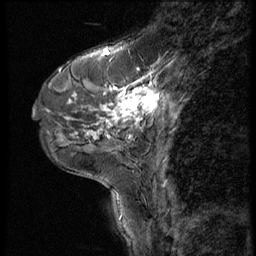
Breast MRI (dynamic contrast-enhanced), one sagittal slice. Slice 21 of 56 in the series (ordered by position). 3 images stored at this slice position (order not interpretable as contrast timing). 1.5 T. TE 4.2 ms, TR 9 ms. 2.5 mm slice thickness. 256 × 256 image matrix. Patient: female, 46 years. From the clinical record (not read from this slice): setting: breast cancer imaged before/during neoadjuvant chemotherapy; receptor status: HER2-positive.
Outlined on this slice (semi-automatic segmentation, software-assisted and operator-edited):
- analysis volume of interest (the breast-tissue region the enhancement analysis was run in; not a lesion): bounding box (x1, y1, x2, y2) in pixels: (79, 68, 190, 143)
- tumour enhancement mask (voxels above the 140 % enhancement threshold inside the analysis volume of interest): (83, 72, 159, 137)